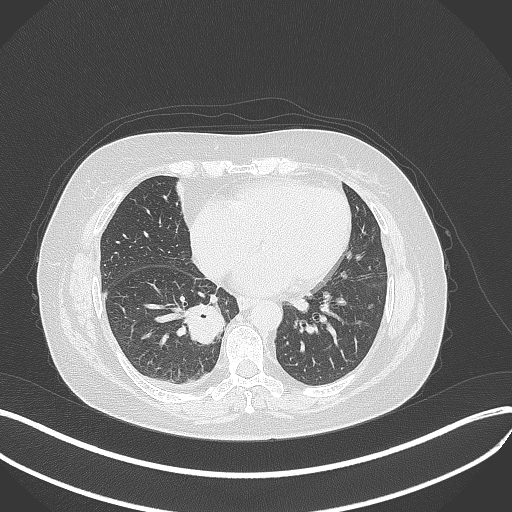
Chest CT, one axial slice; slice 137 of 381 in the series (ordered by position); reconstruction kernel B70f; lung window (W 1500 / L -600 HU); 1 mm slice thickness; 512 × 512 image matrix, field of view 400 × 400 mm. Female patient, age 56 years. From the clinical record (not read from this slice): clinical TNM (as recorded): T2b N1 M0.
Outlined on this slice (rectangle marked by the reading radiologist):
- lung tumour (recorded histology: small cell carcinoma): bounding box [x1, y1, x2, y2] px = [186, 302, 229, 350]